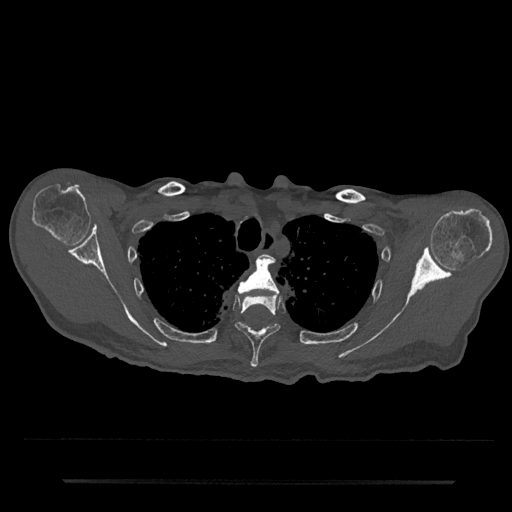
CT including the spine, one axial slice. Position 625 of 797 along the scan axis. Reconstruction kernel Br40s/3. 120 kVp. Bone window (W 1800 / L 400 HU). 0.5 mm slice thickness. 512 × 512 image matrix, field of view 427 × 427 mm. Male patient, age 74 years. Case-level facts recorded for this patient, not image findings: primary cancer: prostate.
Structures marked on this image (semi-automatic segmentation, software-assisted and operator-edited):
- T2 vertebra: bounding box <264,255,268,259> (left, top, right, bottom; pixels)
- T3 vertebra: <237,256,279,296>
- T4 vertebra: <234,294,280,368>